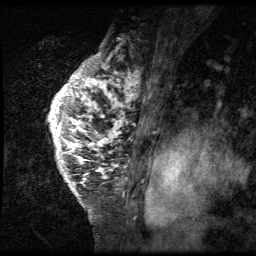
Breast MRI (dynamic contrast-enhanced), one sagittal slice. 3 images stored at this slice position (order not interpretable as contrast timing). 1.5 T. TE 4.2 ms, TR 9 ms. 256 × 256 image matrix, field of view 180 × 180 mm. Female patient, age 50 years. From the clinical record (not read from this slice): setting: breast cancer imaged before/during neoadjuvant chemotherapy; receptor status: triple-negative.
Outlined on this slice (semi-automatic segmentation, software-assisted and operator-edited):
- analysis volume of interest (the breast-tissue region the enhancement analysis was run in; not a lesion): bounding box <32,39,138,212> (left, top, right, bottom; pixels)
- tumour enhancement mask (voxels above the 140 % enhancement threshold inside the analysis volume of interest): <48,53,138,190>